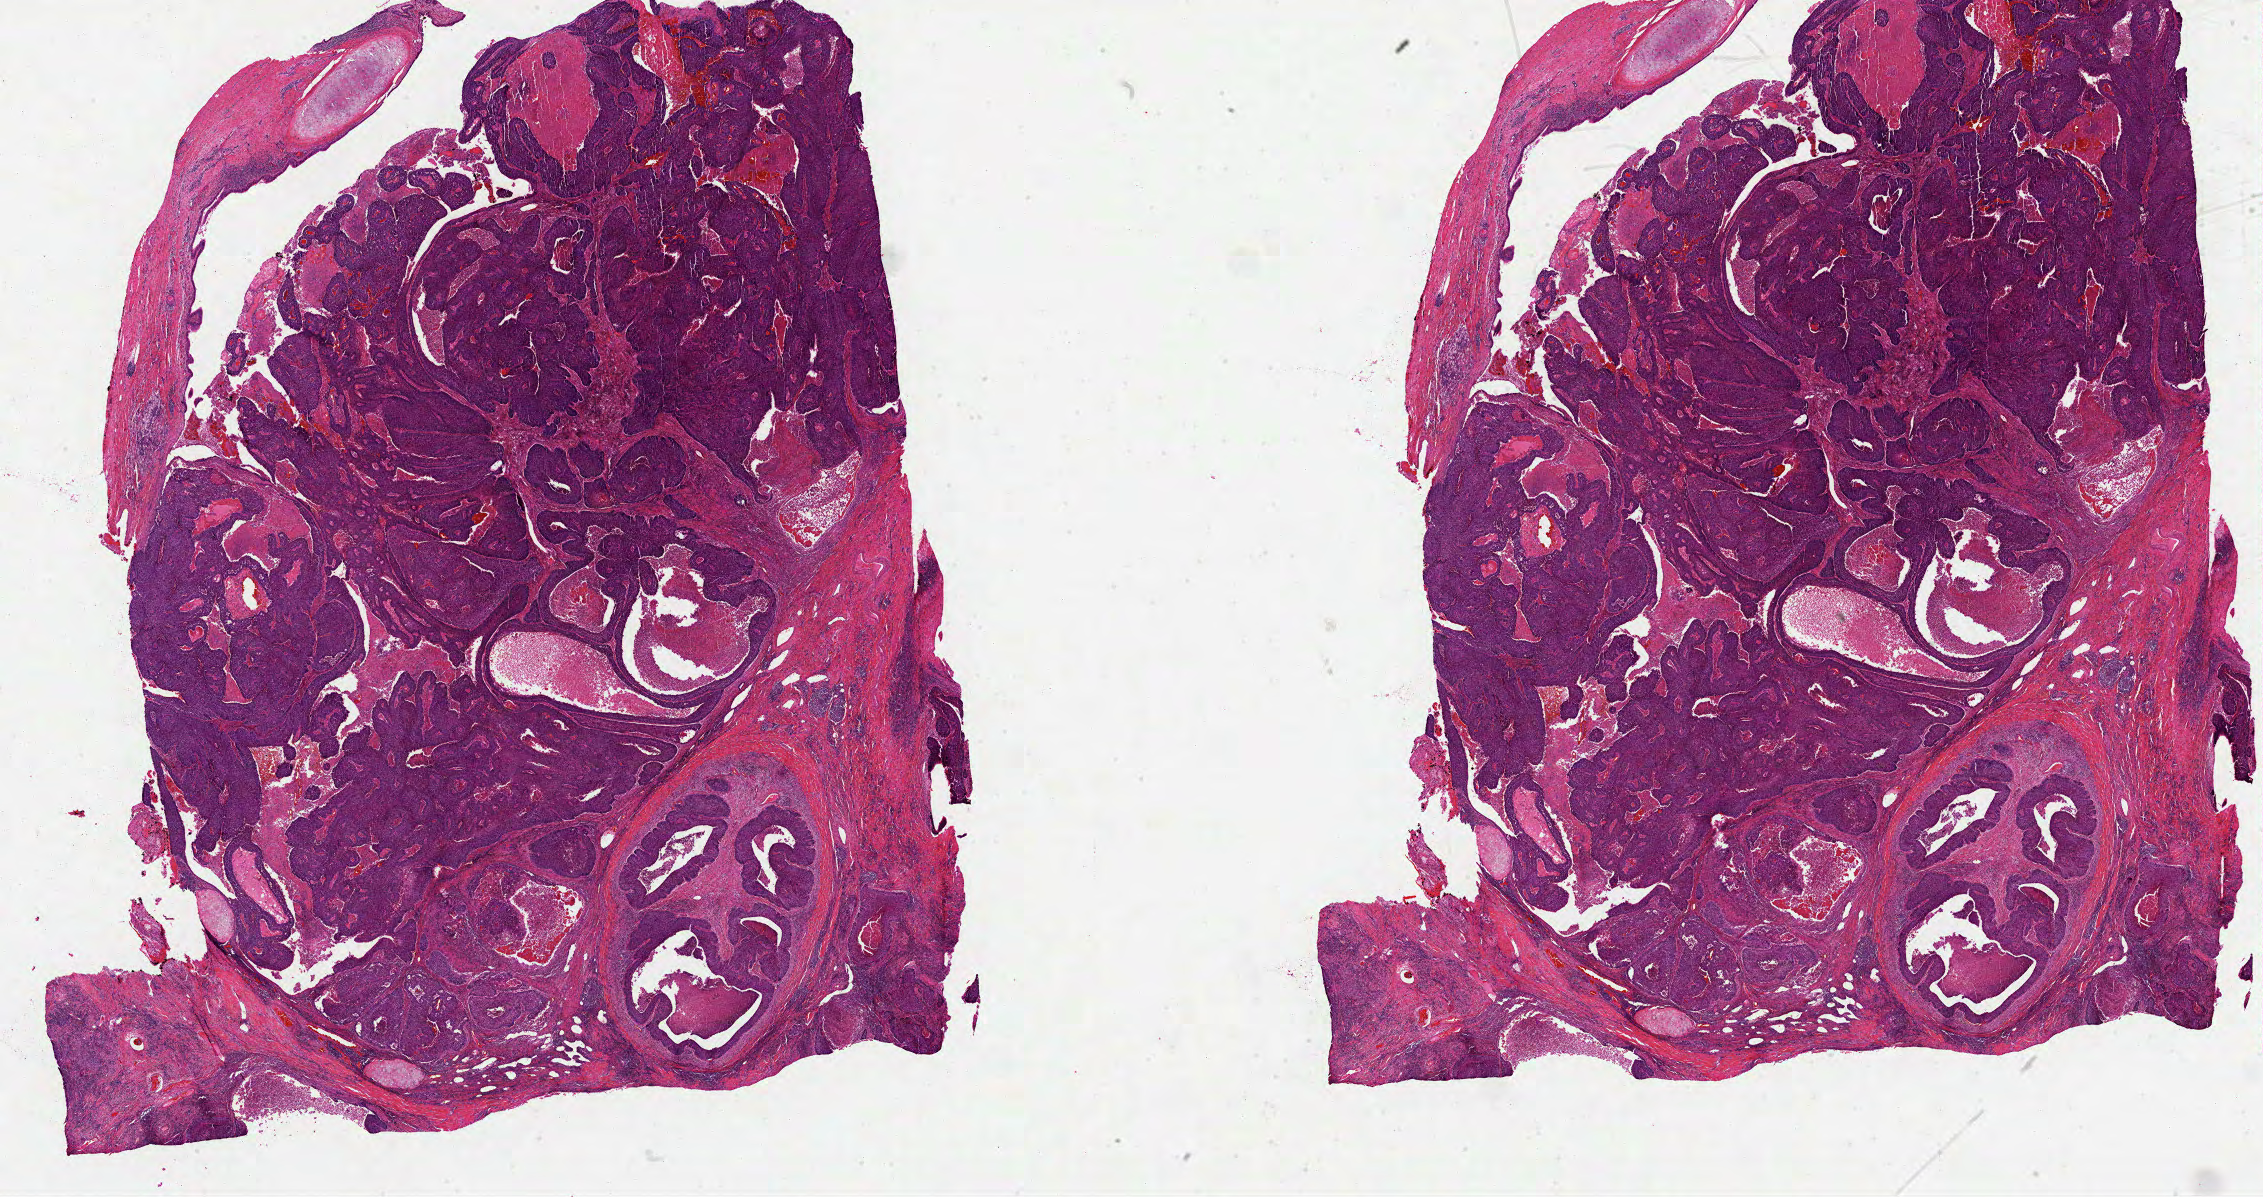
Digitized Hematoxylin and eosin (H&E) stained tissue section (whole slide), whole scanned area (about 36.5 x 19.3 mm, slide scanned at 40x) shown as a low-resolution overview; formalin-fixed paraffin-embedded (FFPE) diagnostic section; sample: primary tumour, lung. Male patient; age at initial diagnosis 66 years.
* pathologic diagnosis: Squamous cell carcinoma, NOS (upper lobe, lung)
* AJCC pathologic stage: IIIA (6th edition)
* TNM: T2 N2 M0